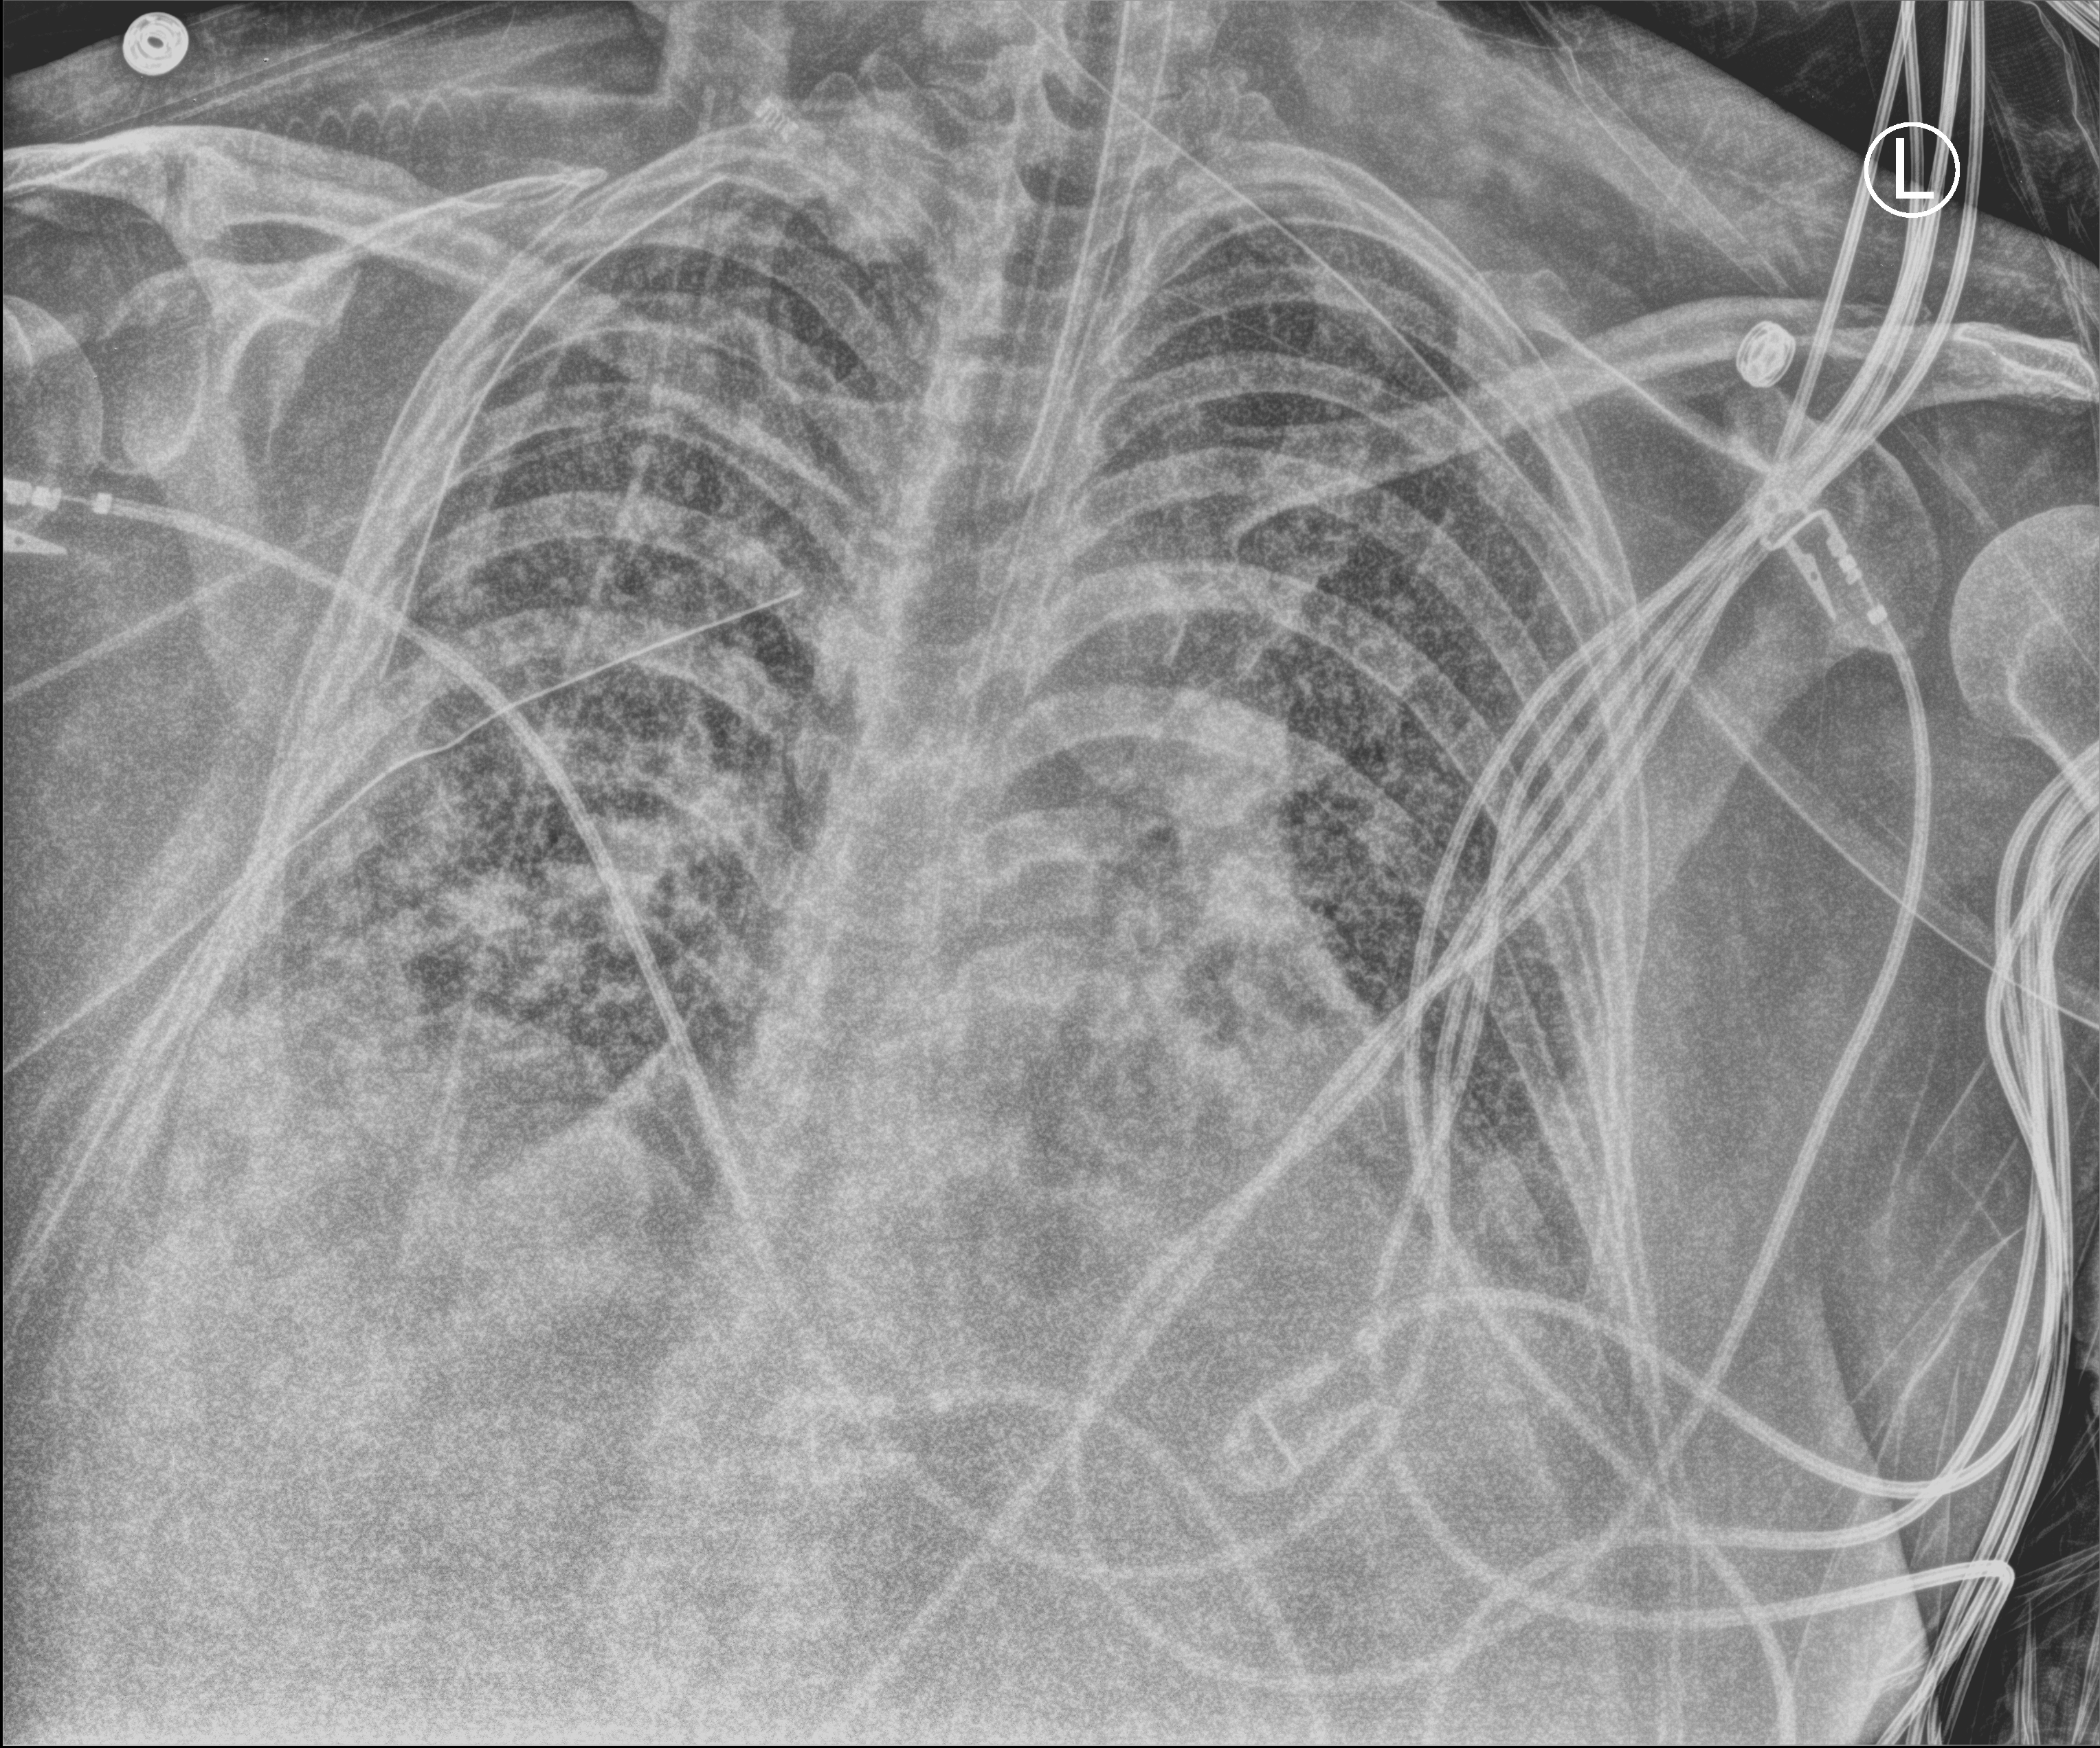
Bedside chest radiograph (computed radiography), anteroposterior (AP) projection. Adult patient hospitalised with COVID-19, age 18–59 years.
Admission-level facts for this patient (not findings on this image; timing relative to this image not recorded): hypertension (admission record): no; mechanically ventilated during this hospital stay: yes; COPD (admission record): no.